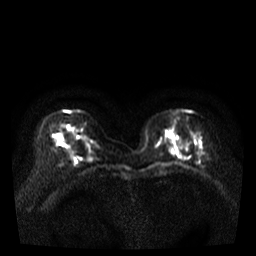
Breast MRI, one axial slice. Position 10 of 35 along the scan axis. Diffusion-weighted series; image 2 of 4 stored at this slice position (different b-values; order by instance number). 3 T. 256 × 256 image matrix, field of view 320 × 320 mm. Female patient.
Annotated regions visible in this slice (outlined manually by an expert reader):
- tumour on diffusion-weighted imaging: bounding box <175,152,182,156> (left, top, right, bottom; pixels)